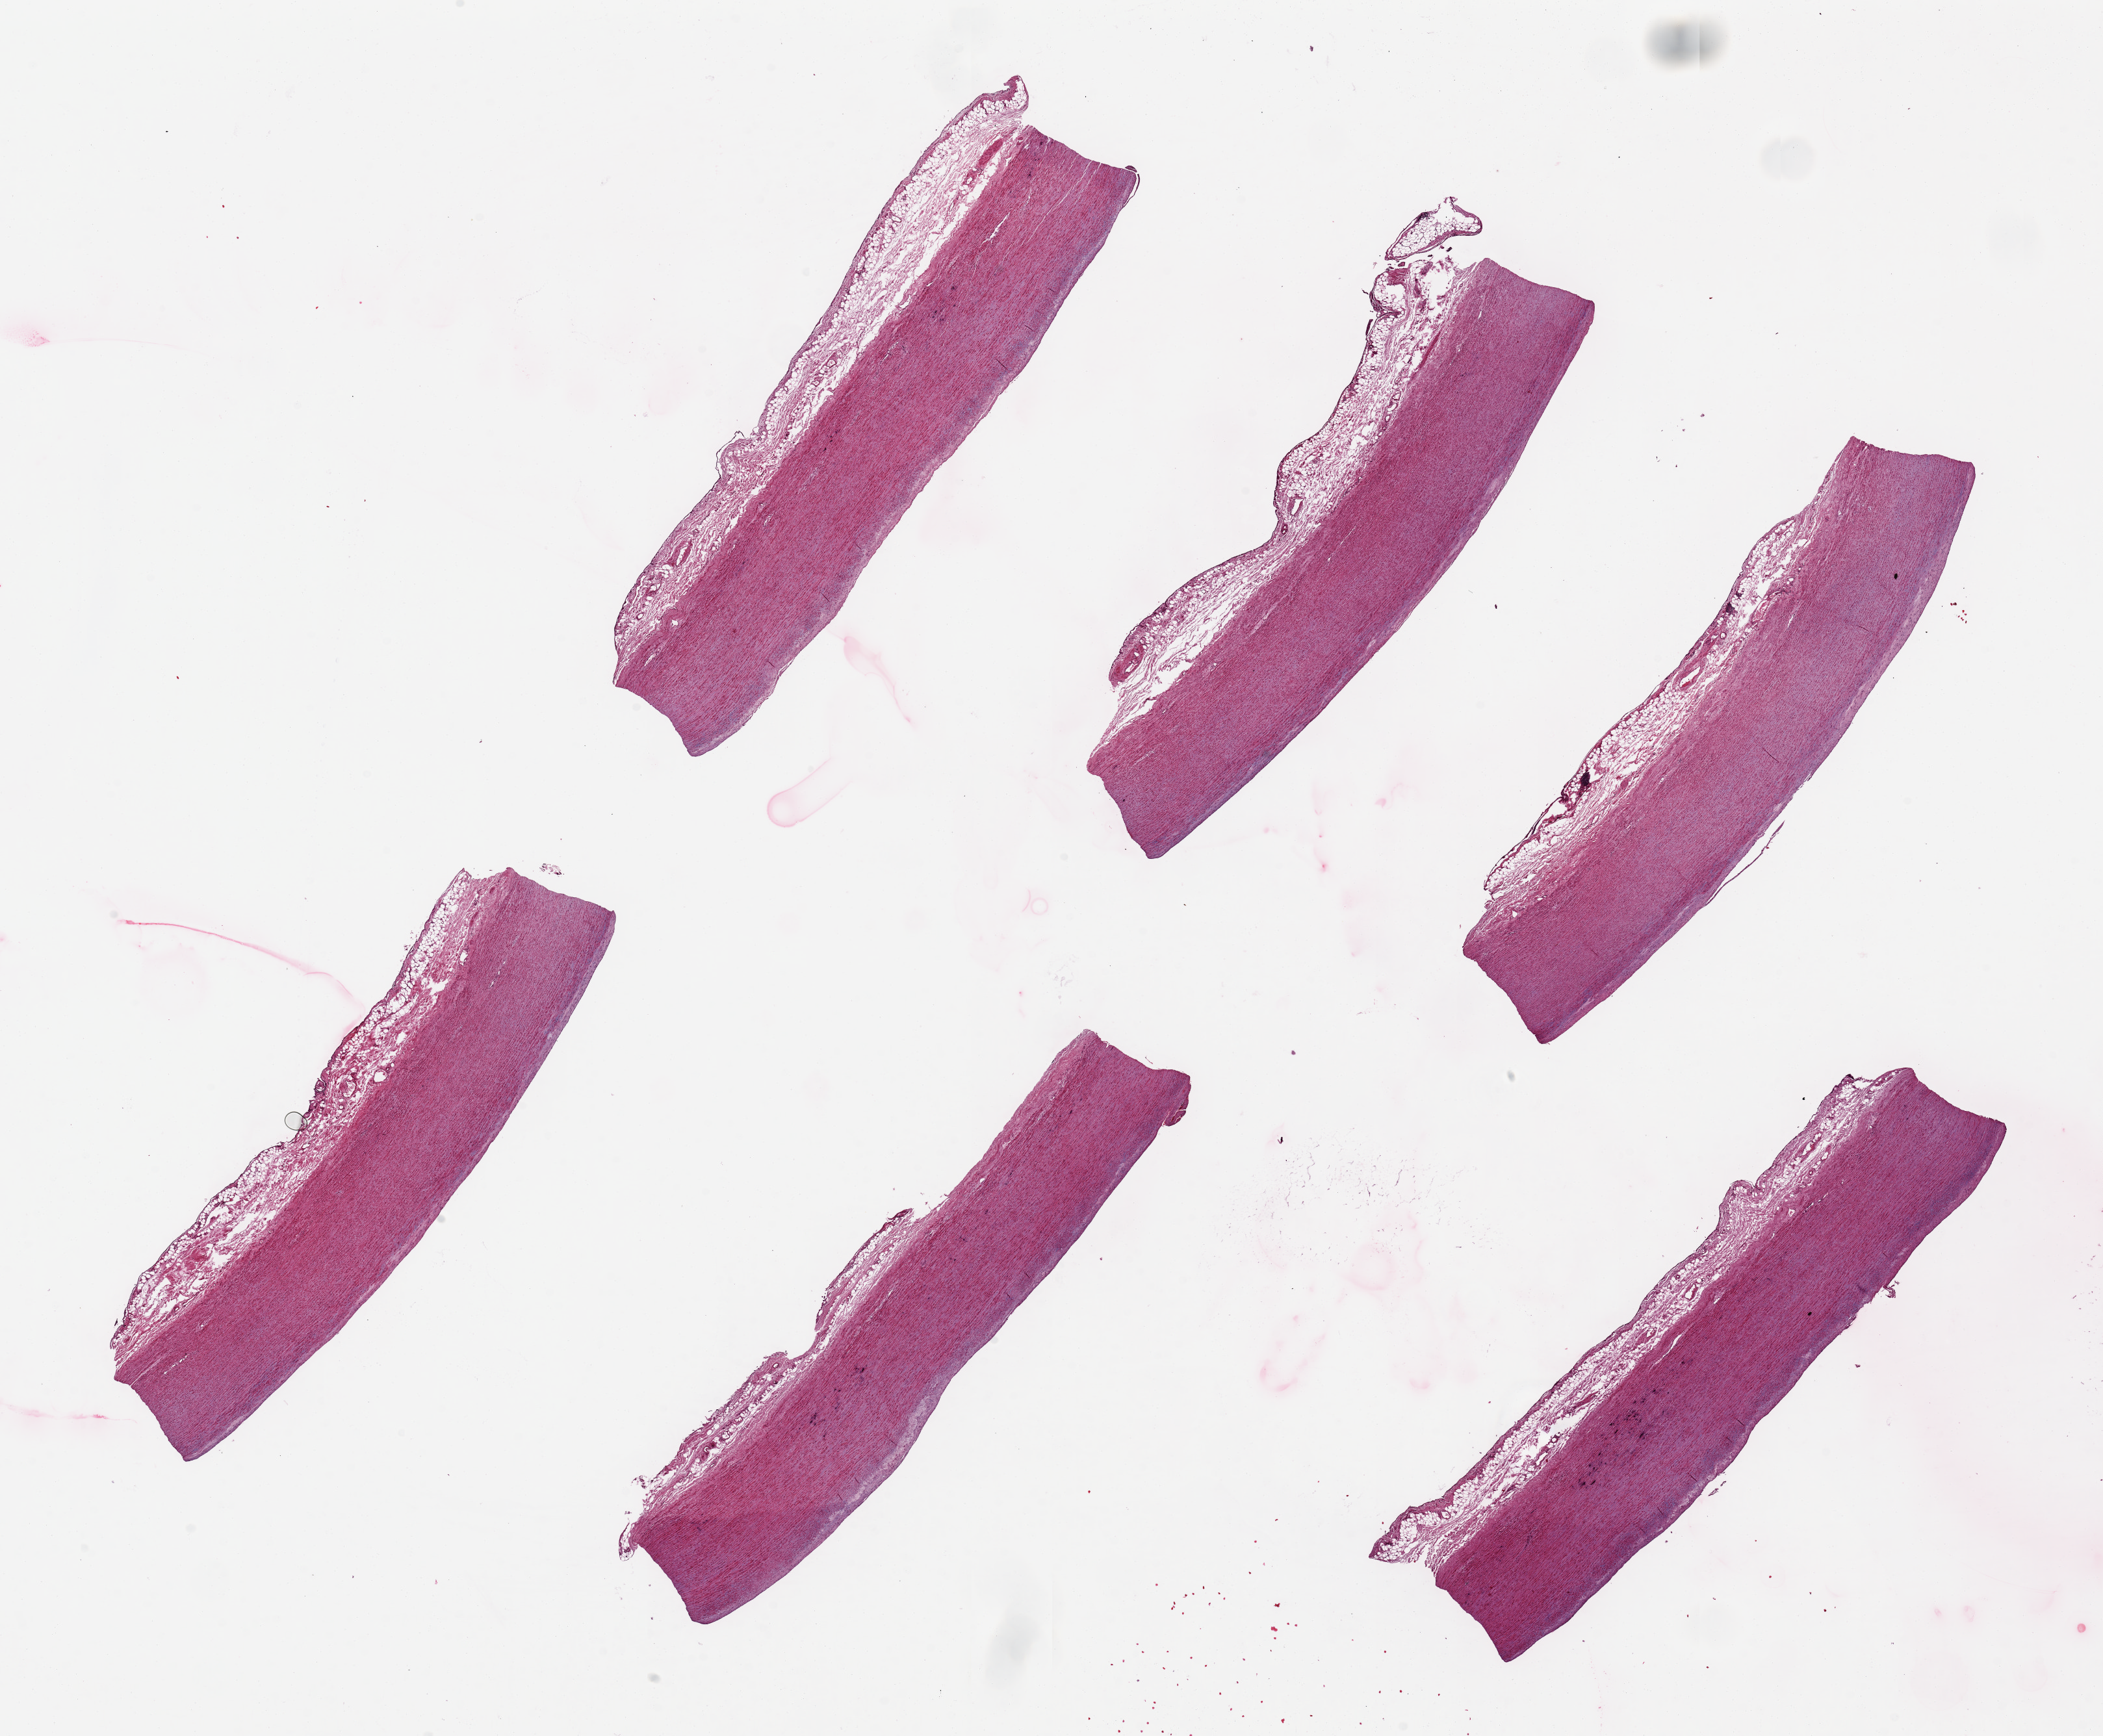
Hematoxylin and eosin (H&E) whole-slide image — a low-resolution overview of the entire scanned area, about 25.6 x 21.1 mm. PAXgene-fixed, paraffin-embedded tissue. Section of aorta (target tissue). Donor tissue sample. Male donor.
Reviewer comment on this tissue sample: 6 pieces up to 9x2 mm; minimal plaque; minimal adventitial adipose.